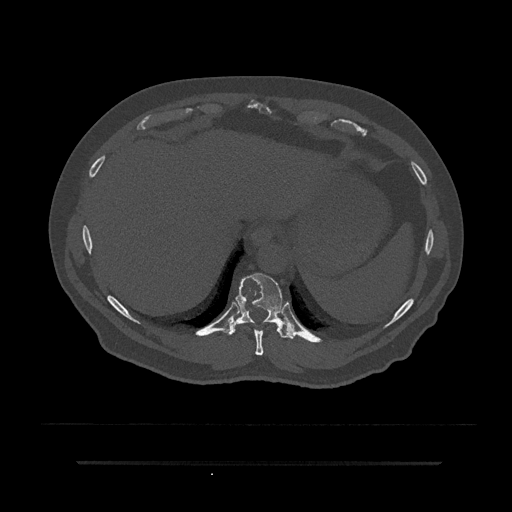
CT including the spine, one axial slice; slice 346 of 797 in the series (ordered by position); reconstruction kernel Br40s/3; bone window (W 1800 / L 400 HU); 512 × 512 image matrix, field of view 464 × 464 mm. Patient: male, 59 years. Case-level facts recorded for this patient, not image findings: primary cancer: bile ducts; vertebrae with lytic lesions (as recorded): T10.
Outlined on this slice (semi-automatic segmentation, software-assisted and operator-edited):
- T10 vertebra: bounding box [x1, y1, x2, y2] px = [227, 273, 295, 339]
- T9 vertebra: [254, 329, 264, 355]